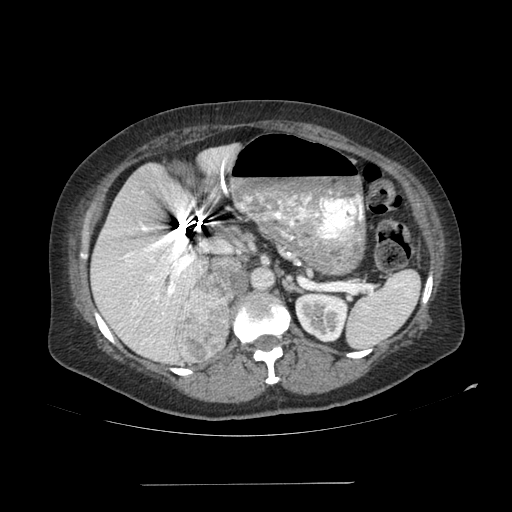
Contrast-enhanced abdominal CT, one axial slice. Slice 62 of 113 in the series (ordered by position). 120 kVp. Soft-tissue window (W 400 / L 40 HU). 512 × 512 image matrix, field of view 440 × 440 mm. Patient: female, 67 years. Case-level facts recorded for this patient, not image findings: diagnosis: adrenocortical carcinoma; tumour side: right adrenal; tumour size at pathology: 9.8 cm; Ki-67 index: 59 %; stage (as recorded): 4.
Annotated regions visible in this slice (semi-automatic segmentation, software-assisted and operator-edited):
- mass: bounding box <177,274,235,362> (left, top, right, bottom; pixels)